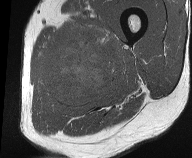
MRI of an extremity soft-tissue mass, one axial slice. Slice 19 of 61 in the series (ordered by position). MR volume resampled by the dataset authors to the PET/CT grid (not the native acquisition matrix). 3.27 mm slice thickness. 192 × 158 image matrix. Male patient. From the clinical record (not read from this slice): histological type: pleiomorphic liposarcoma; grade: high; site of the primary tumour: left thigh.
Annotated regions visible in this slice (expert contour drawn on MRI and transferred to this co-registered scan by the dataset authors):
- gross tumour volume including surrounding oedema: box from (x=39, y=21) to (x=126, y=111) px
- gross tumour volume (mass): (x=45, y=37)–(x=112, y=106)